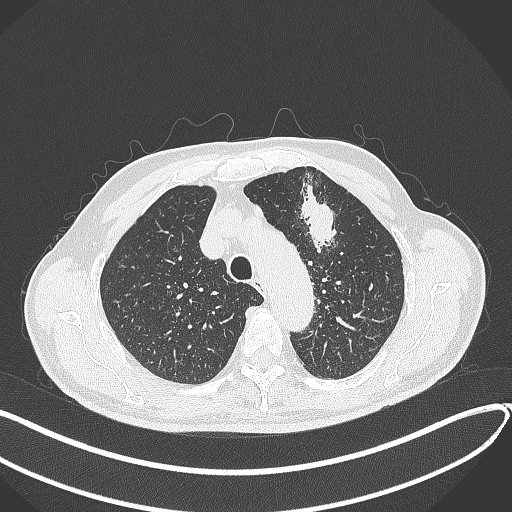
Chest CT, one axial slice. Reconstruction kernel B70f. 120 kVp. Lung window (W 1500 / L -600 HU). 512 × 512 image matrix, field of view 400 × 400 mm. Patient: male, 74 years. Case-level facts recorded for this patient, not image findings: clinical TNM (as recorded): T2b N0 M1c.
Outlined on this slice (bounding box drawn by a radiologist):
- lung tumour (recorded histology: adenocarcinoma): bounding box (x1, y1, x2, y2) in pixels: (291, 178, 342, 255)